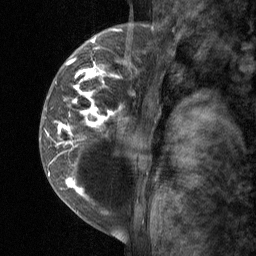
Breast MRI (dynamic contrast-enhanced), one sagittal slice; position 17 of 64 along the scan axis; dynamic contrast-enhanced study with each time point stored as its own series, time point 2 of 3 at this slice position (early post-contrast, ordered by acquisition time); 1.5 T; TE 4.8 ms, TR 27 ms; 2 mm slice thickness; 256 × 256 image matrix, field of view 180 × 180 mm. Patient: female, 34 years. Case-level facts recorded for this patient, not image findings: setting: breast cancer imaged before/during neoadjuvant chemotherapy; receptor status: HR-positive, HER2-negative.
Structures marked on this image (semi-automatically segmented with operator editing):
- analysis volume of interest (the breast-tissue region the enhancement analysis was run in; not a lesion): bounding box (x1, y1, x2, y2) in pixels: (41, 23, 157, 197)
- tumour enhancement mask (voxels above the 90 % enhancement threshold inside the analysis volume of interest): (45, 30, 134, 196)